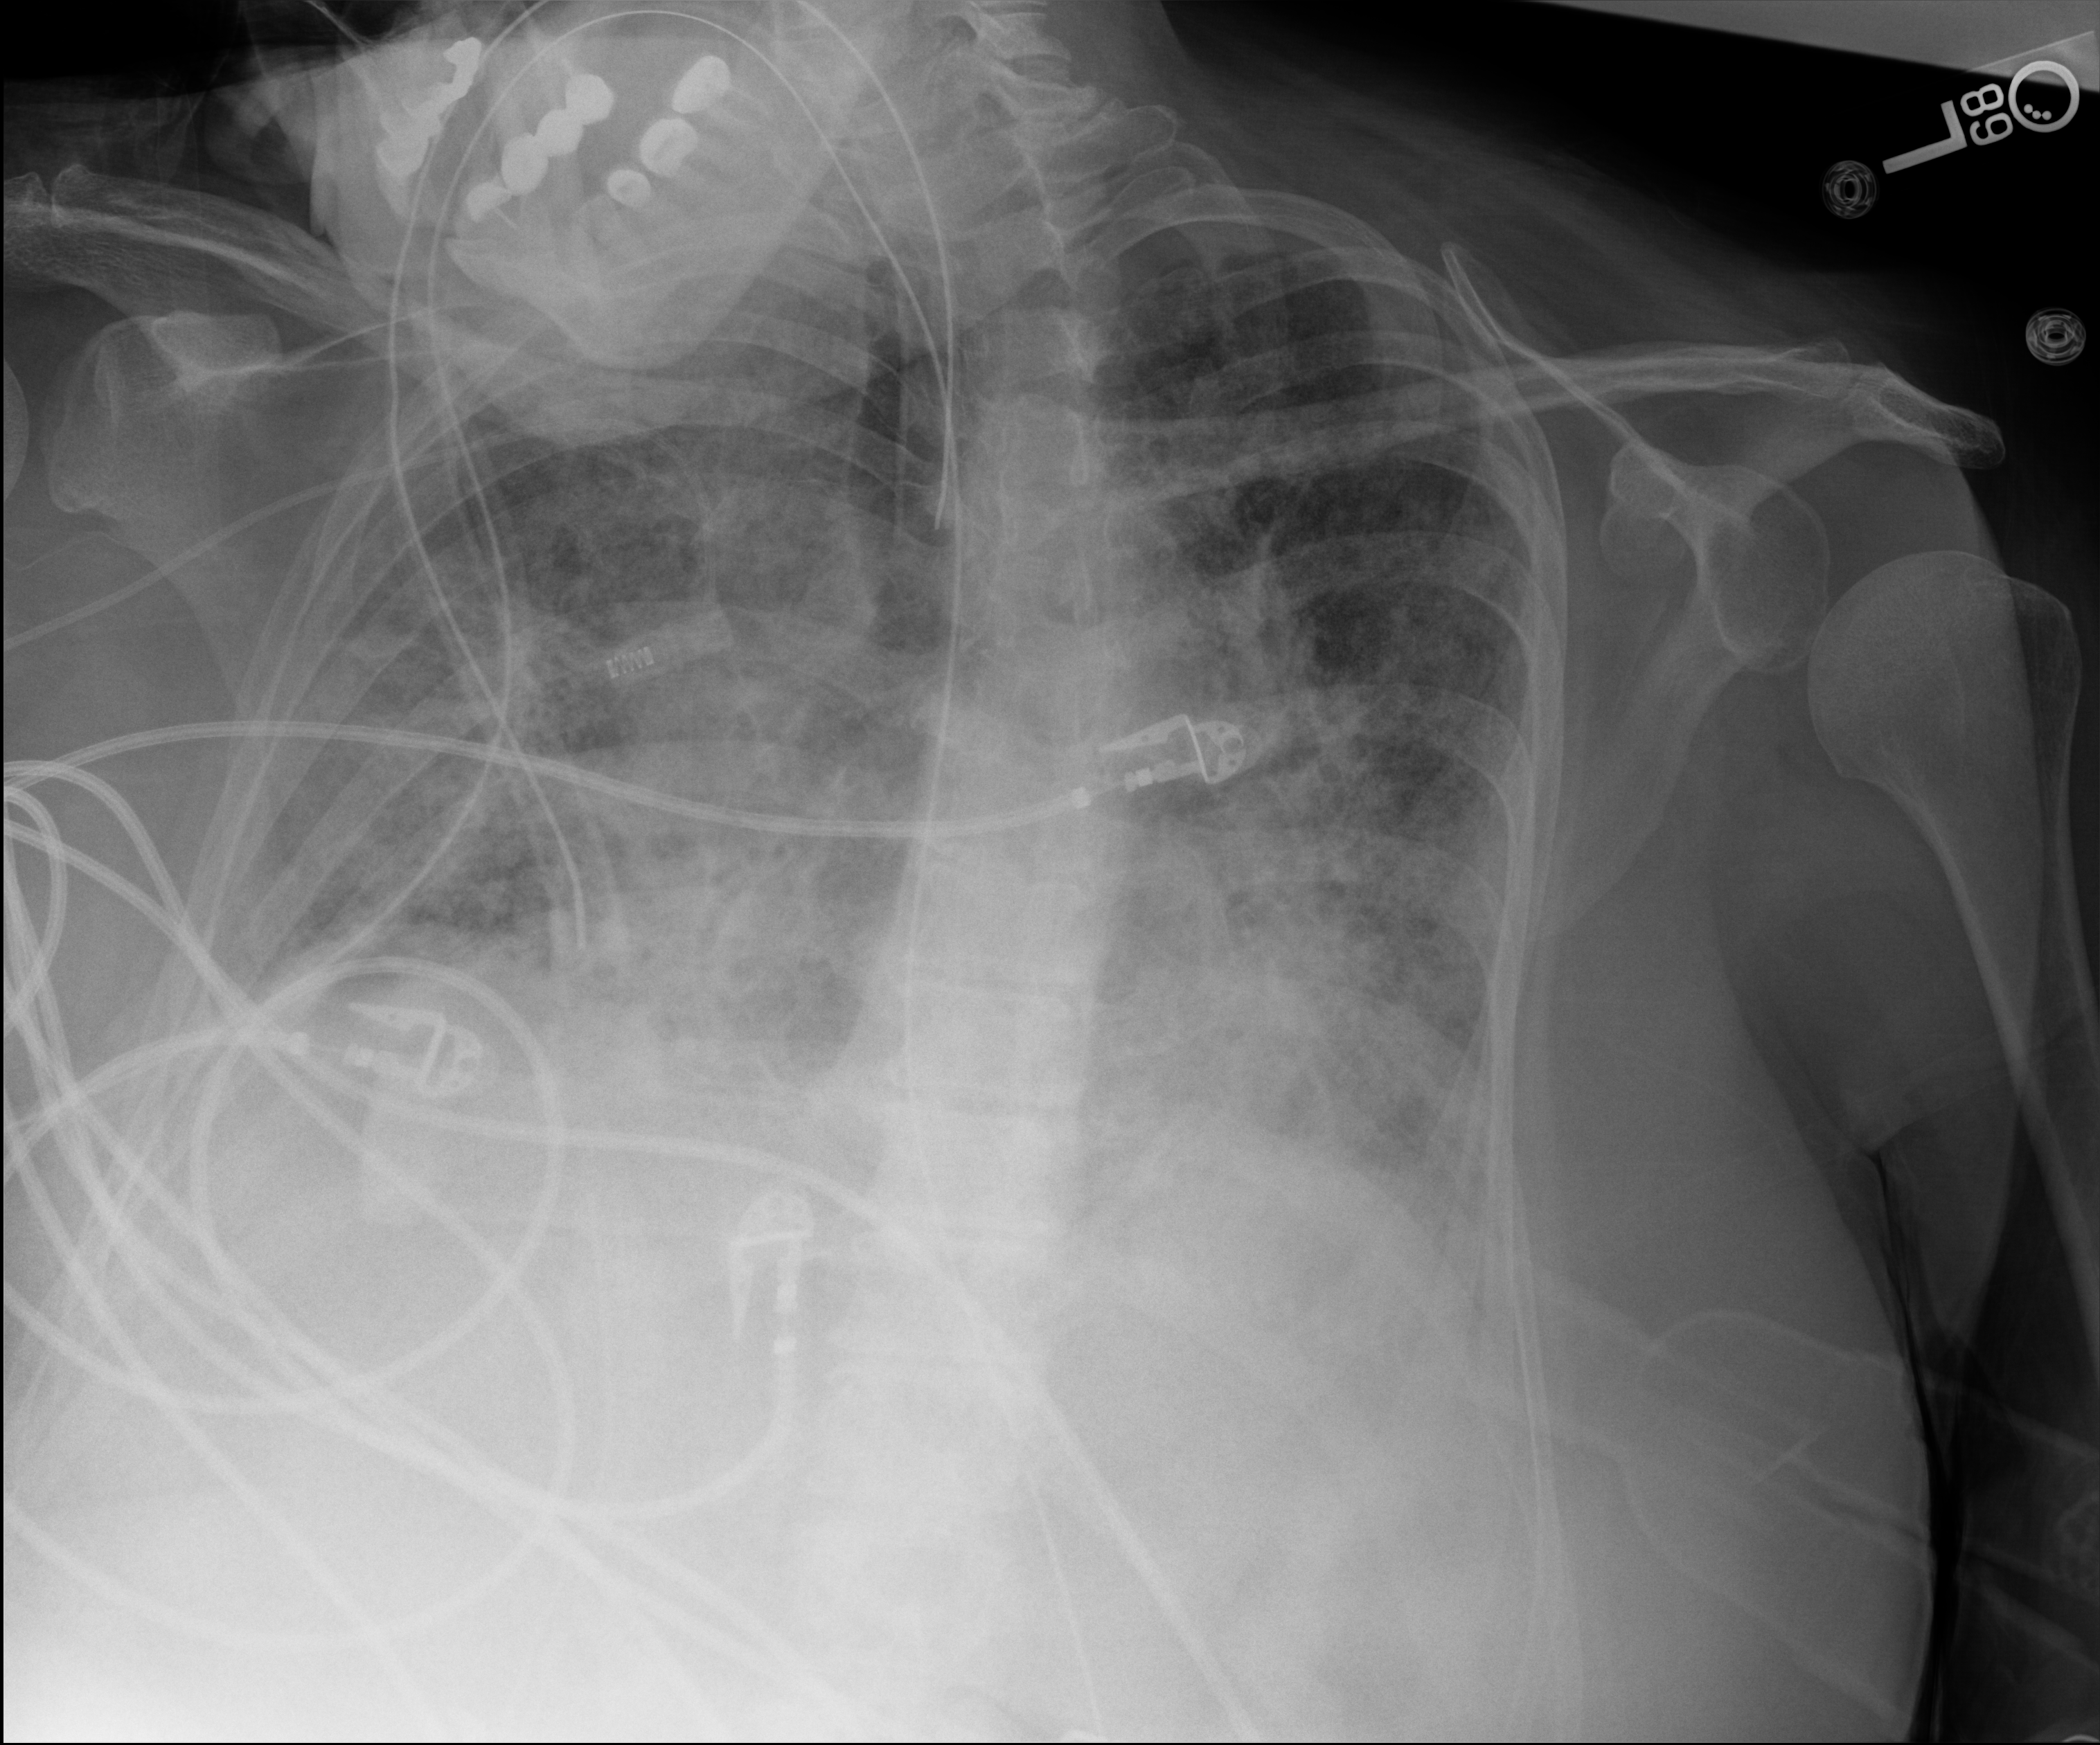
Bedside chest radiograph (digital radiography), anteroposterior (AP) projection. Patient hospitalised with COVID-19; female, aged 60–74 years.
Admission-level facts for this patient (not findings on this image; timing relative to this image not recorded): mechanically ventilated during this hospital stay: yes; diabetes (admission record): no.